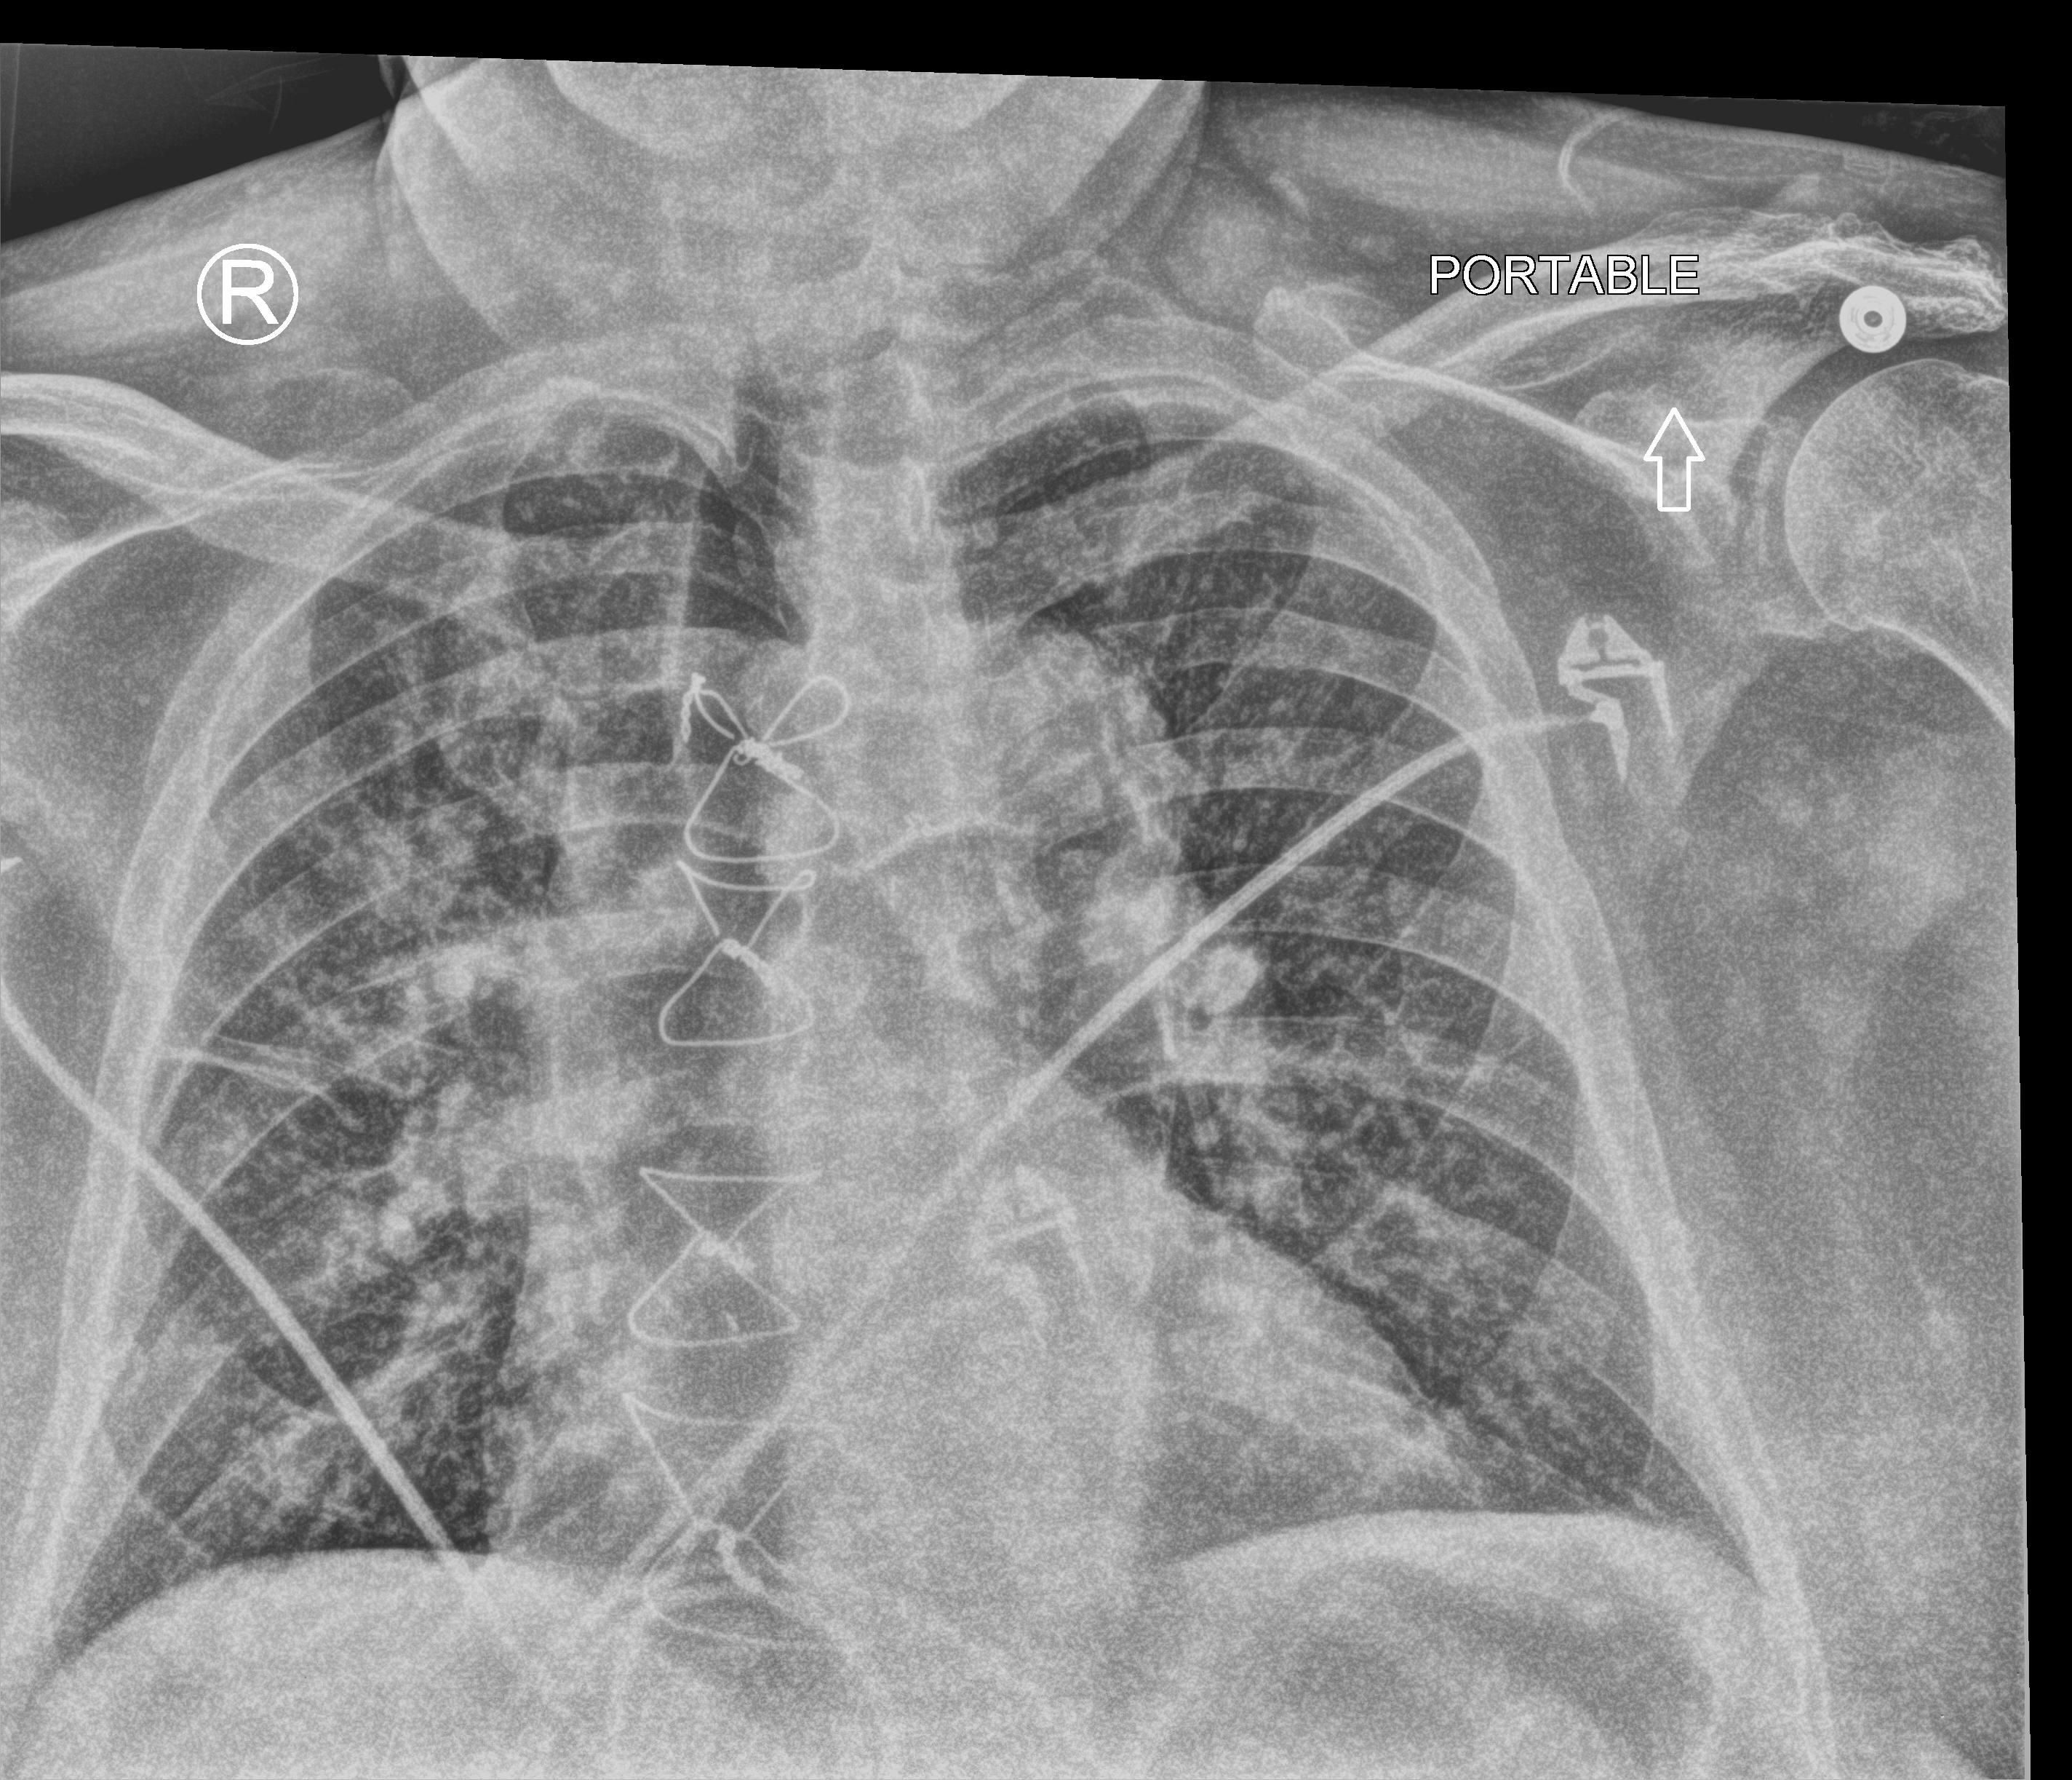
Portable chest radiograph; anteroposterior (AP) projection. Patient hospitalised with COVID-19; male, aged 75–90 years.
Admission-level facts for this patient (not findings on this image; timing relative to this image not recorded): mechanically ventilated during this hospital stay: no; length of hospital stay: 9 days.